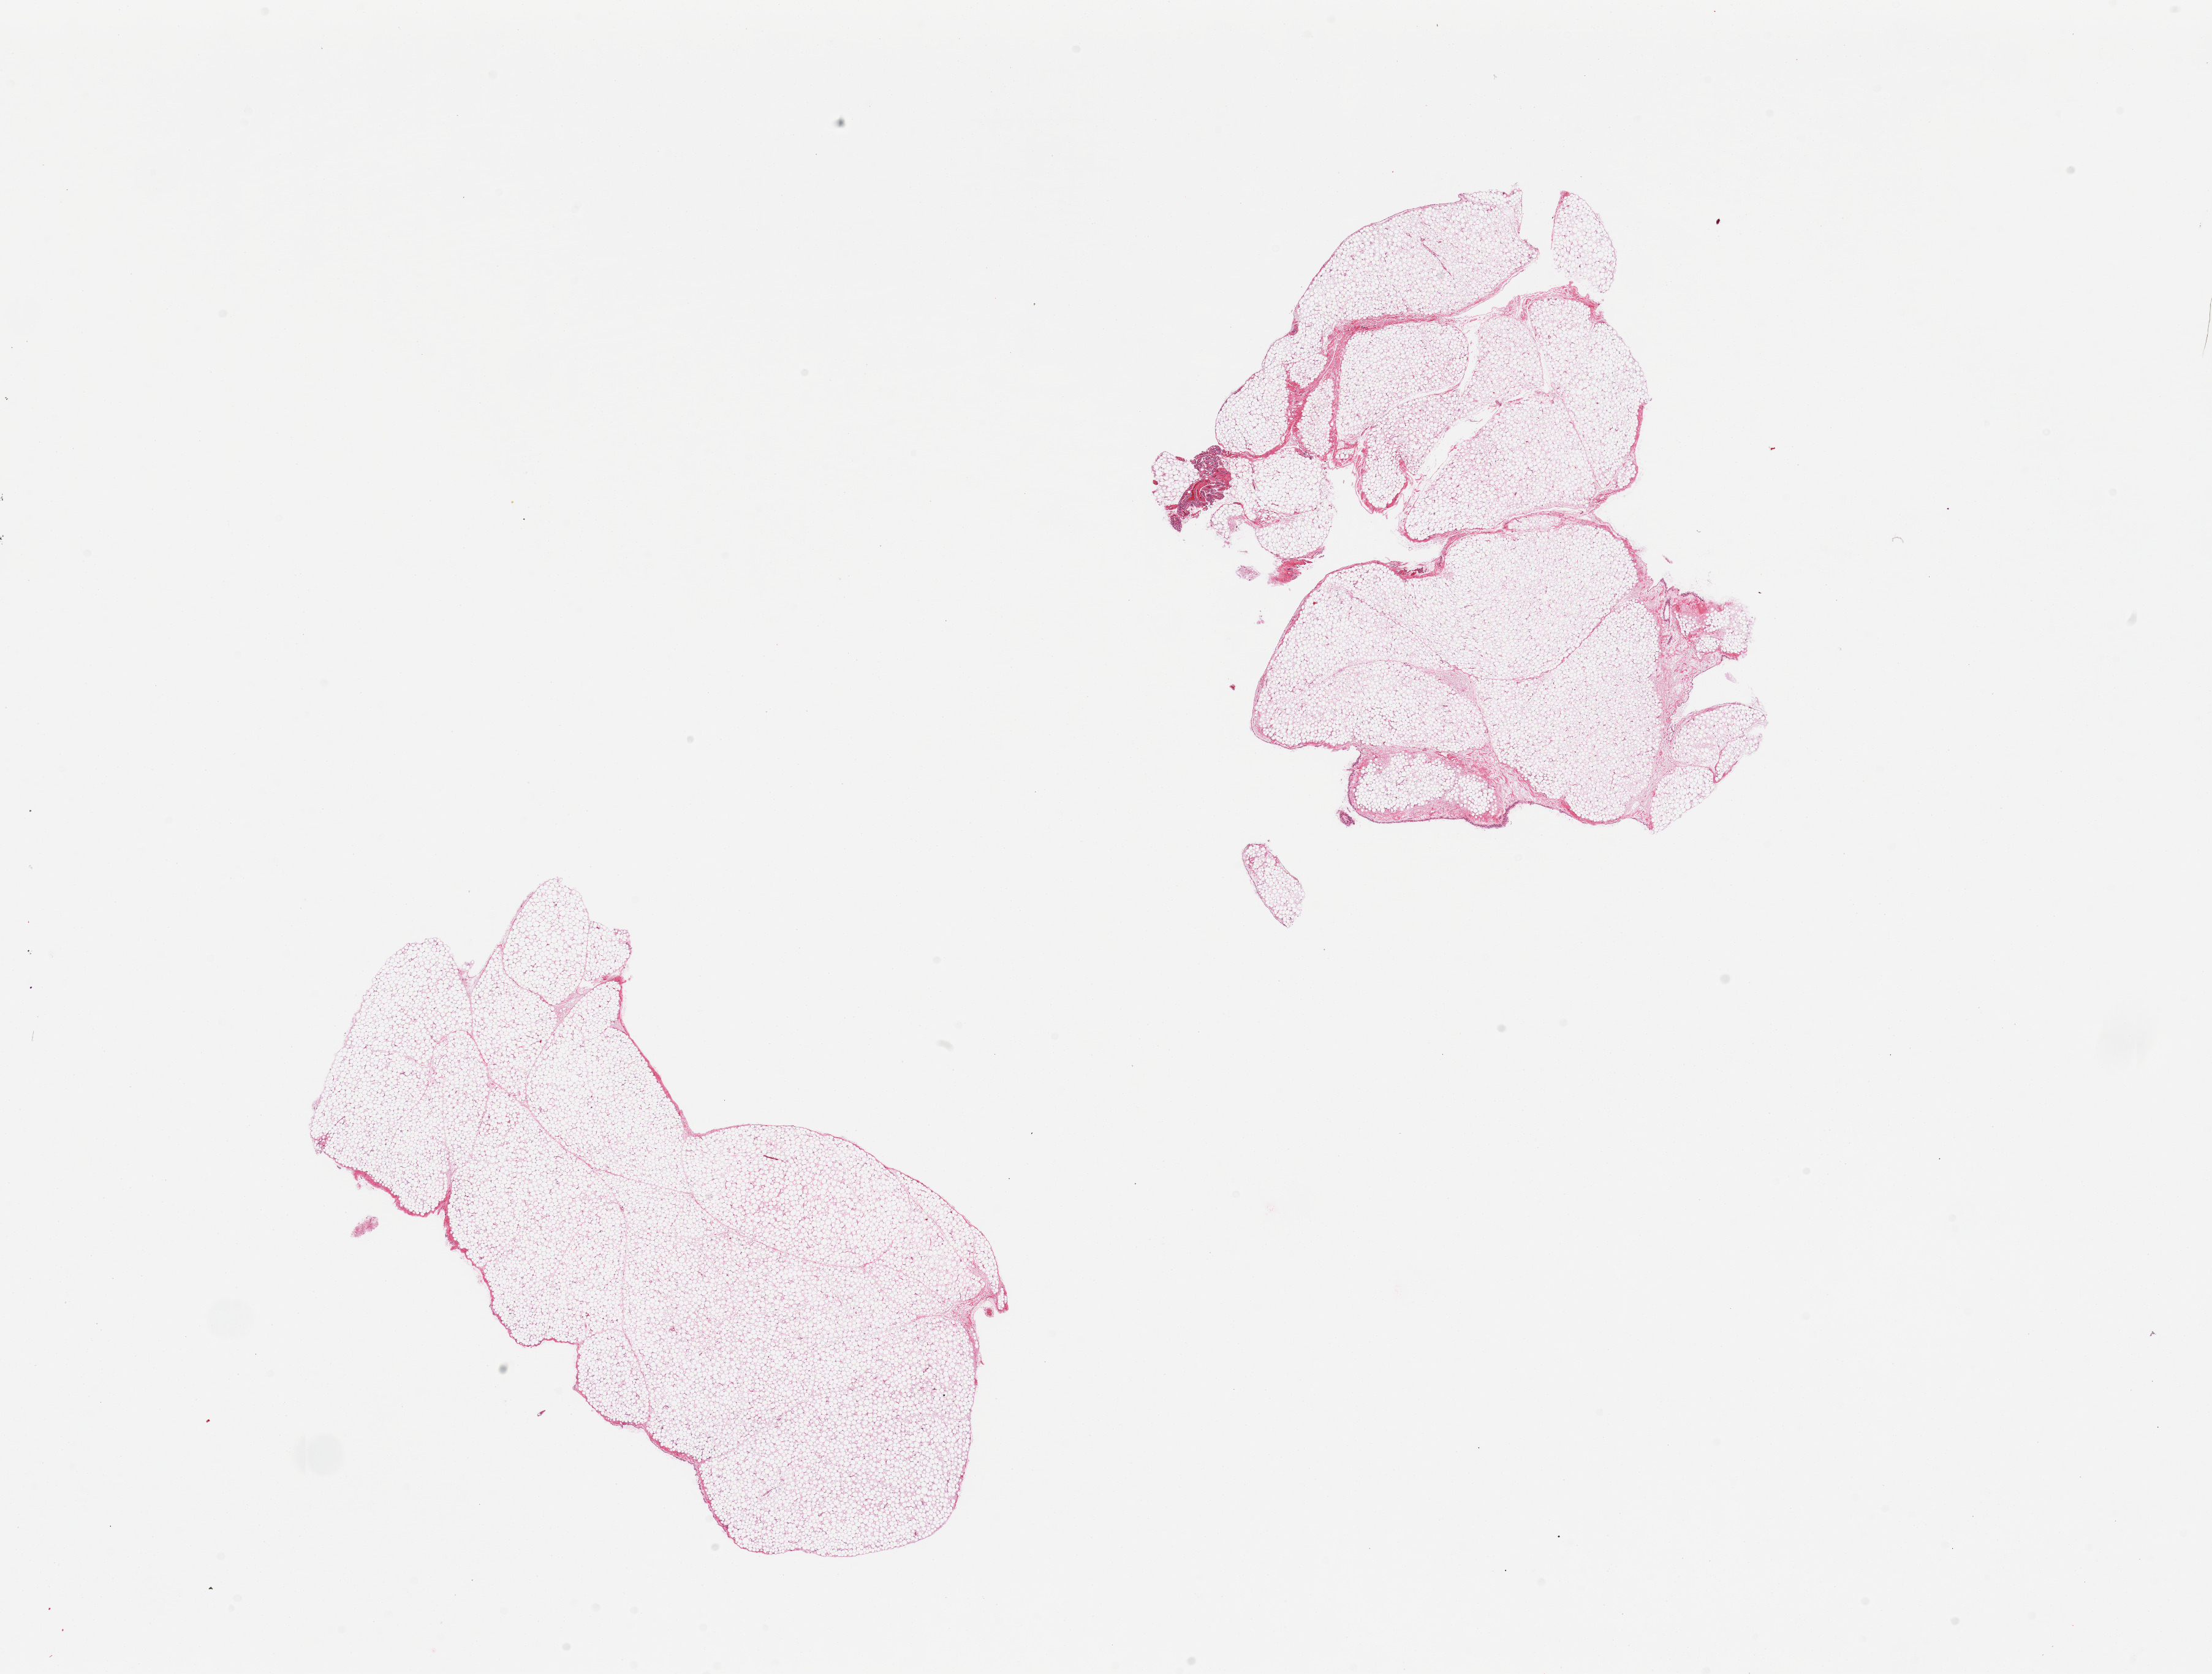
Haematoxylin and eosin whole-slide image, low-resolution overview of the scanned area, about 28.5 x 21.6 mm, PAXgene-fixed, paraffin-embedded tissue, sampled site (target tissue): omentum, donor tissue sample.
Pathologist's review note for this sample: 2 pieces, minimal fibrous or vascular tissue, go specimens.